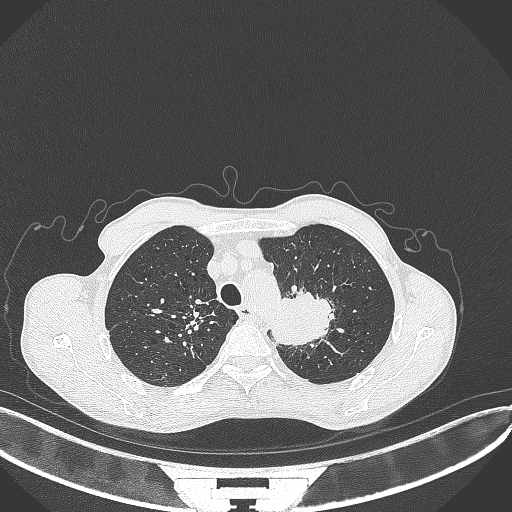
Chest CT, one axial slice; slice 339 of 386 in the series (ordered by position); reconstruction kernel B70f; lung window (W 1500 / L -600 HU); 1 mm slice thickness; 512 × 512 image matrix. Male patient, age 65 years. From the clinical record (not read from this slice): clinical TNM (as recorded): T2b N0 M0; histopathological grade: G2.
Outlined on this slice (bounding box drawn by a radiologist):
- lung tumour (recorded histology: adenocarcinoma): box from (x=270, y=284) to (x=339, y=345) px